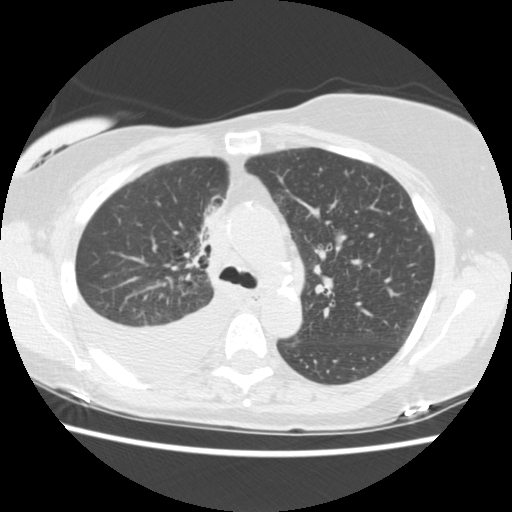
Low-dose screening chest CT, one axial slice. Slice 102 of 157 in the series (ordered by position). Reconstruction kernel STANDARD. 120 kVp. Lung window (W 1500 / L -600 HU). 2.5 mm slice thickness. 512 × 512 image matrix, field of view 330 × 330 mm.
Outlined on this slice (outlined manually by an expert reader):
- lesion 1 (tumor, upper lobe of right lung): bounding box (x1, y1, x2, y2) in pixels: (203, 208, 225, 230)